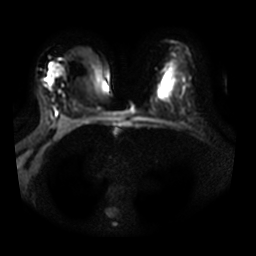
Breast MRI, one axial slice; diffusion-weighted series; image 2 of 4 stored at this slice position (different b-values; order by instance number); 3 T; 256 × 256 image matrix, field of view 350 × 350 mm. Female patient.
Structures marked on this image (outlined manually by an expert reader):
- tumour on diffusion-weighted imaging: bounding box [x1, y1, x2, y2] px = [49, 64, 60, 81]